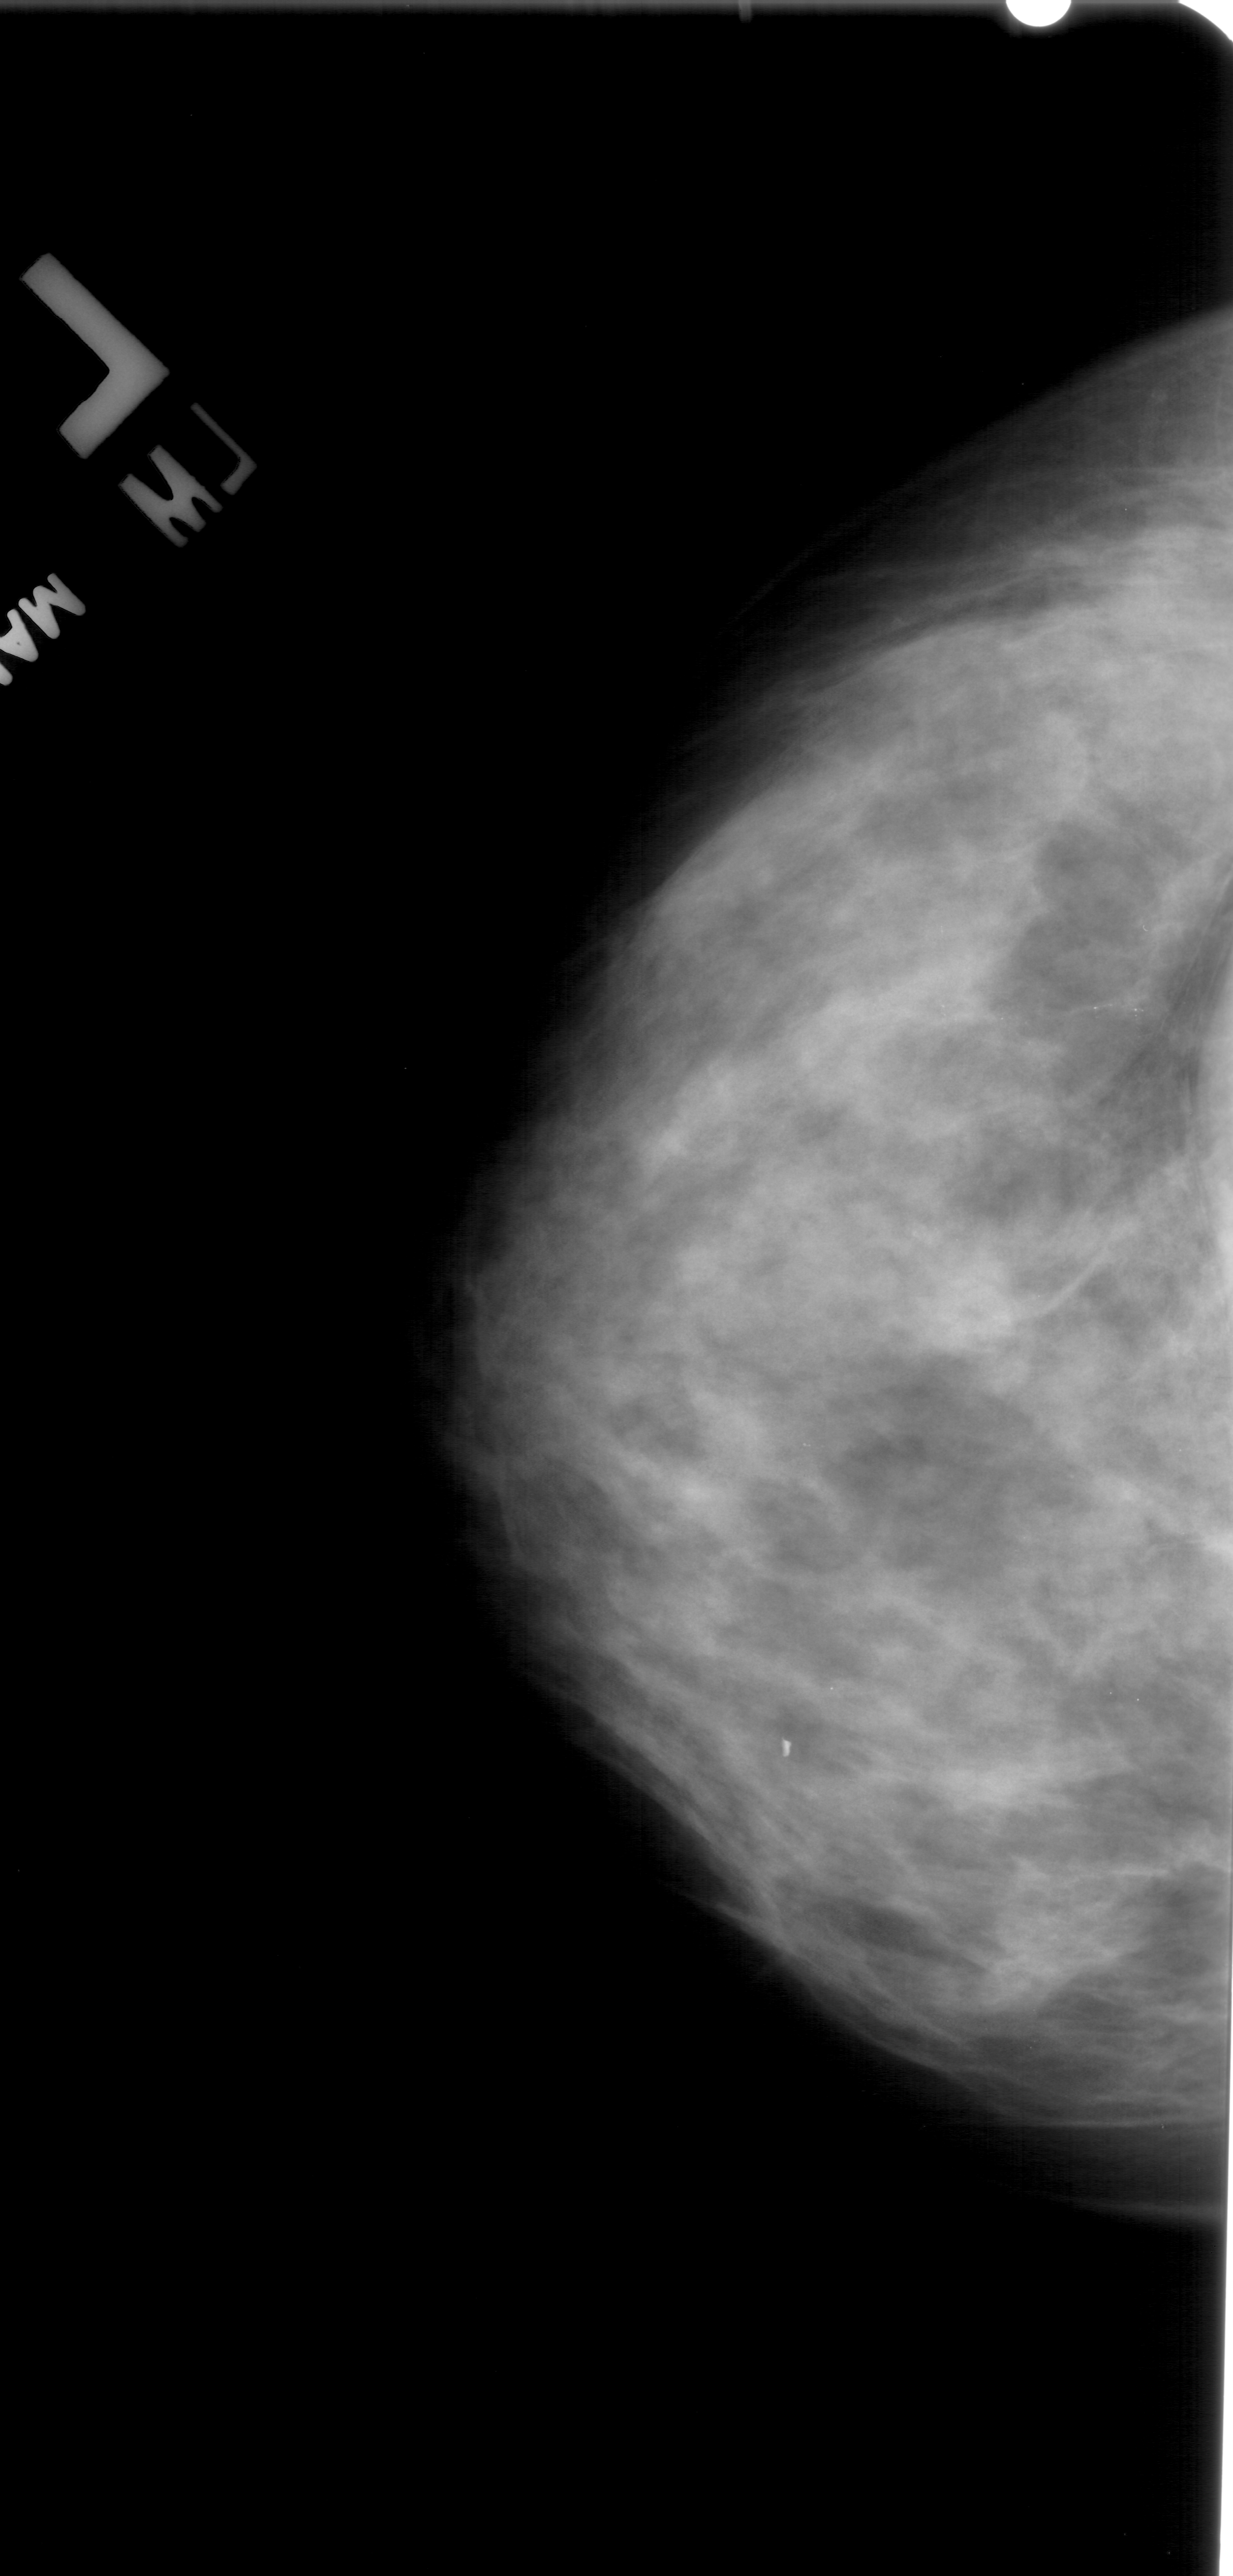
Mammogram (digitized film), left breast, CC view, BI-RADS breast density category 4 (scale 1–4).
Calcifications, morphology pleomorphic, distribution clustered; BI-RADS assessment category 4; pathology result (as recorded, not read from the image): benign.